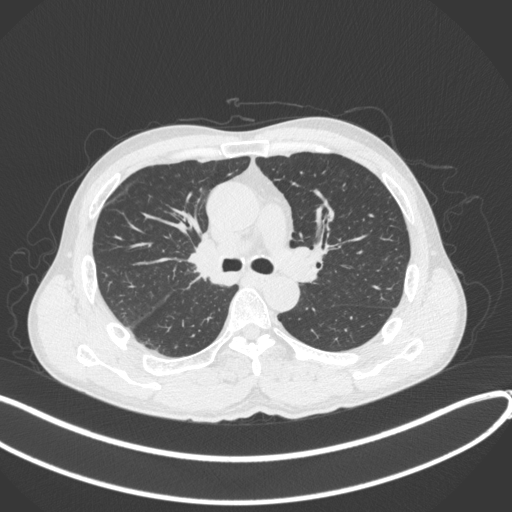
Chest CT, one axial slice. Slice 241 of 409 in the series (ordered by position). Reconstruction kernel B31f. 120 kVp. Lung window (W 1500 / L -600 HU). 1 mm slice thickness. 512 × 512 image matrix, field of view 400 × 400 mm. Patient: male, 53 years. Case-level facts recorded for this patient, not image findings: clinical TNM (as recorded): T1b N0 M0.
Outlined on this slice (bounding box drawn by a radiologist):
- lung tumour (recorded histology: squamous cell carcinoma): bounding box (x1, y1, x2, y2) in pixels: (183, 232, 222, 281)